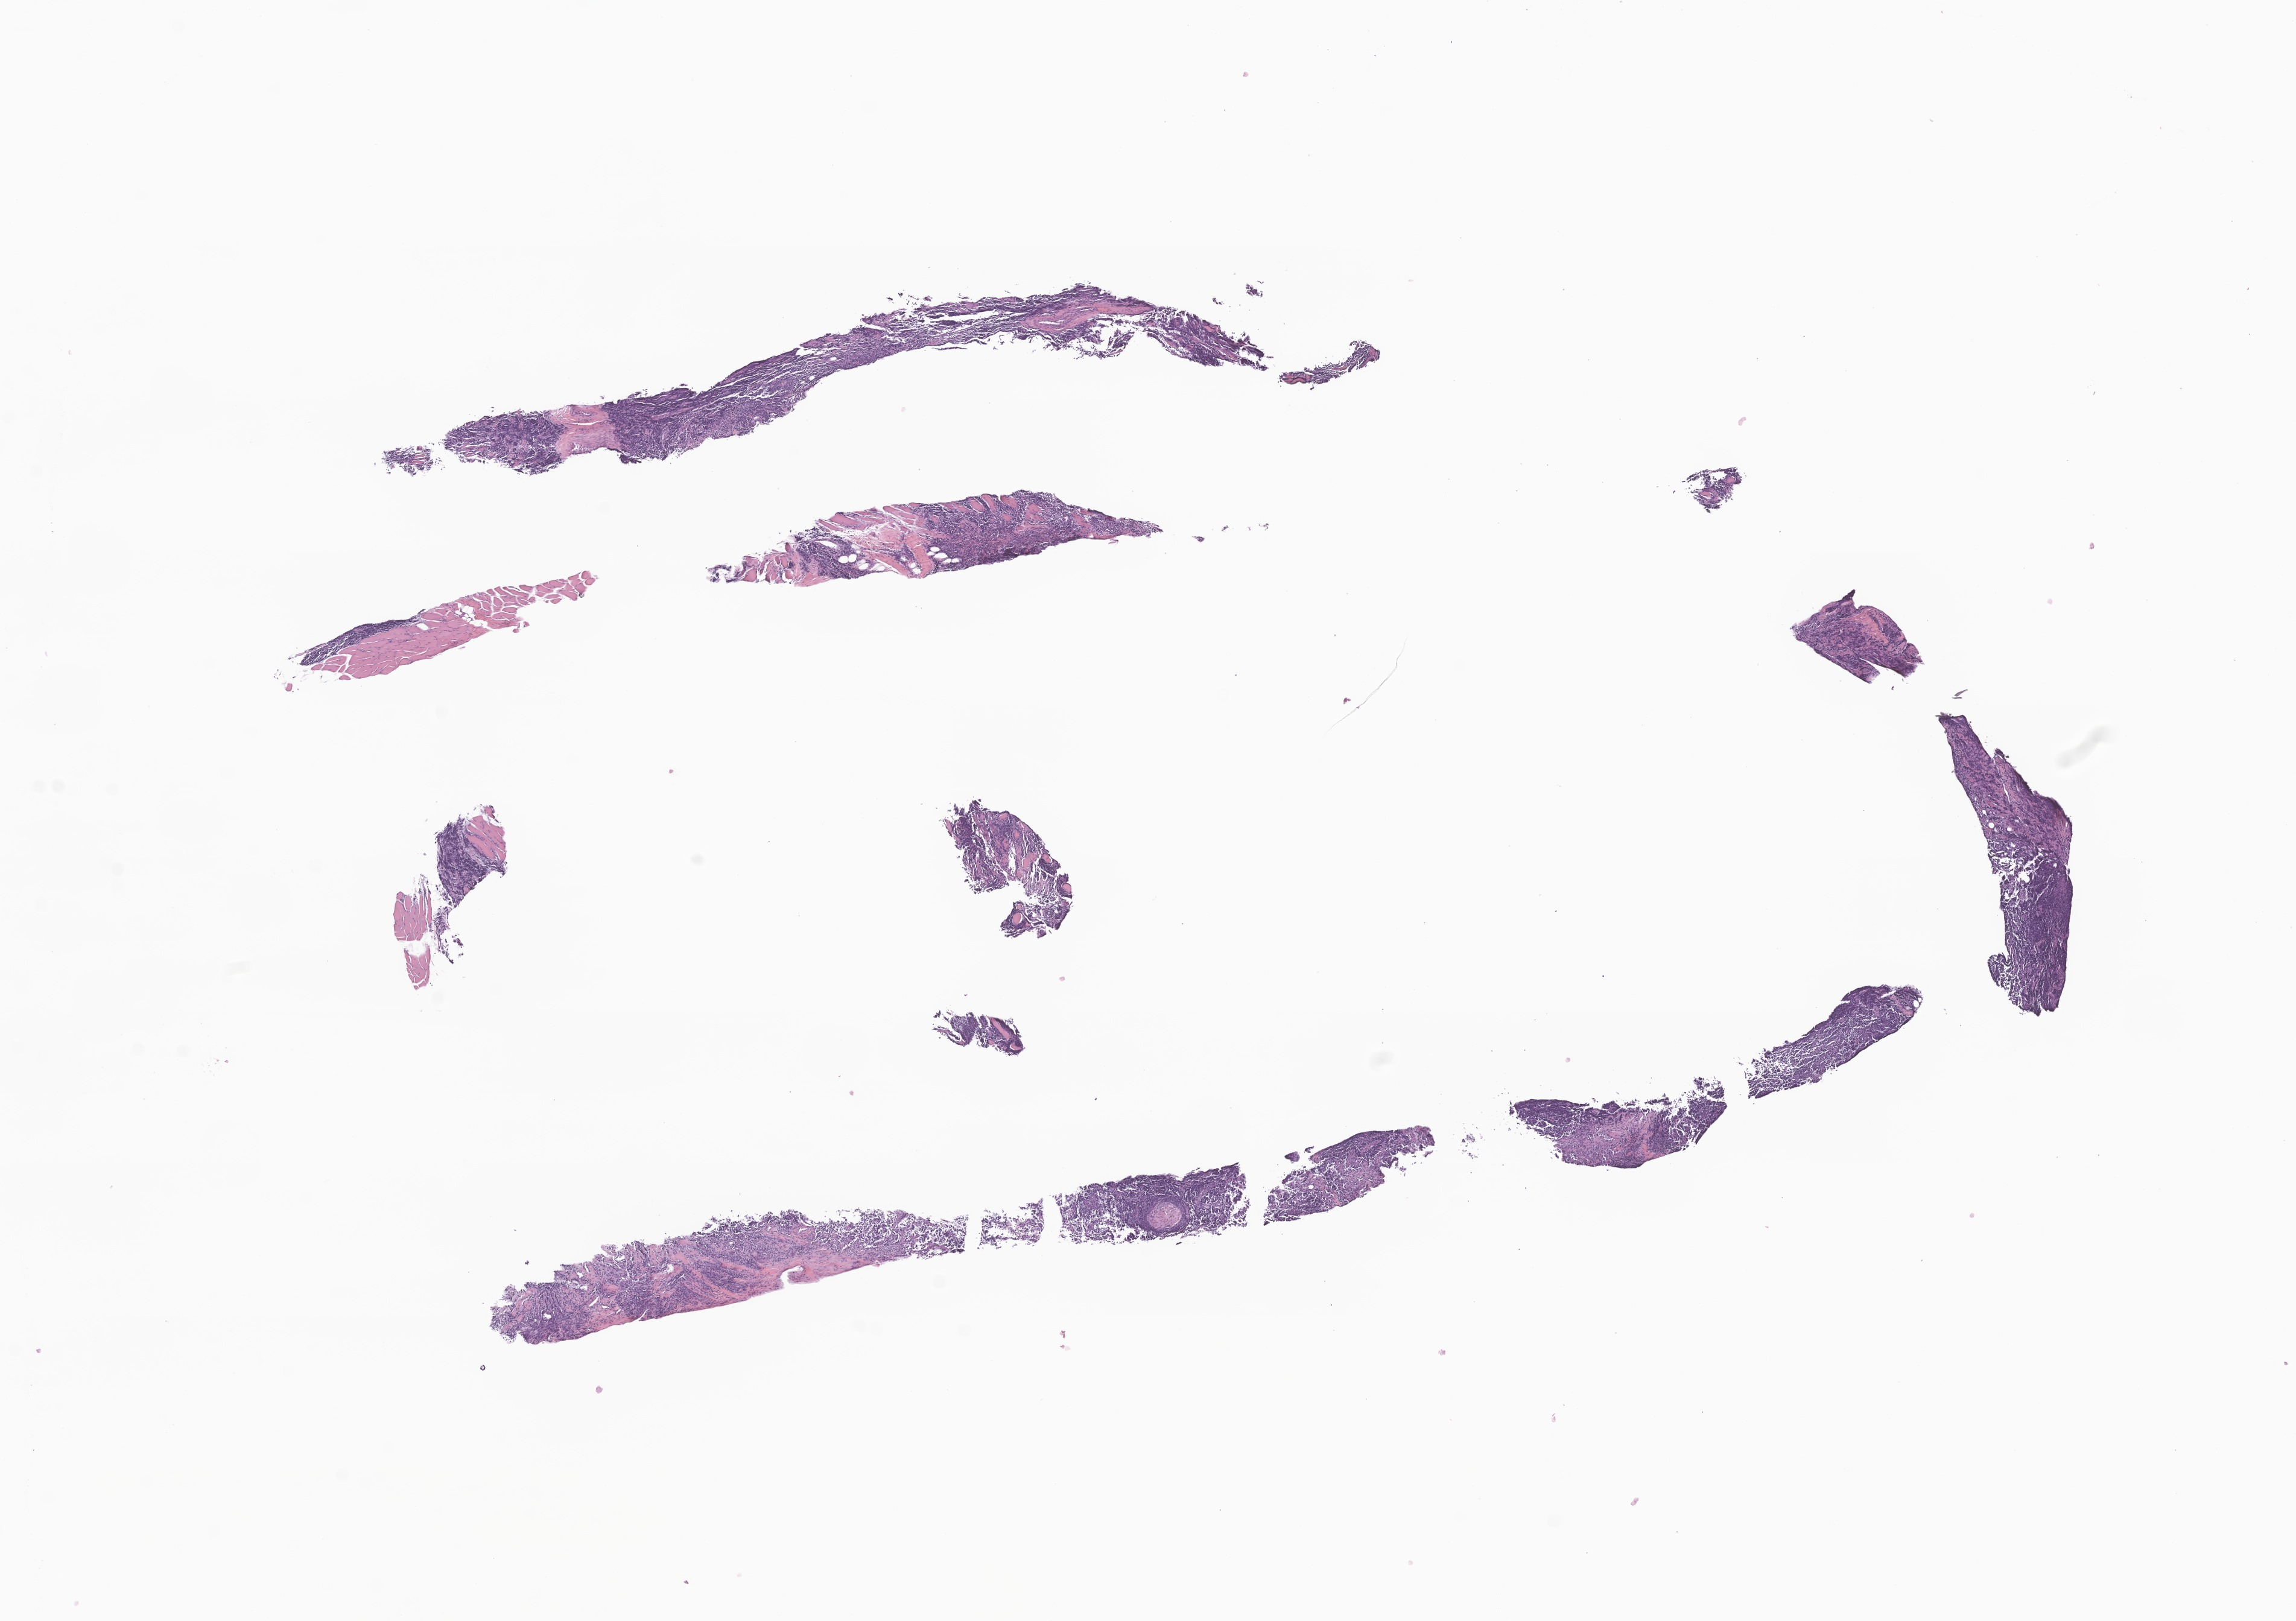
Whole-slide image, H&E stain of tumor tissue from the retroperitoneum — low-resolution overview of the scanned area, about 16.0 x 11.3 mm; formalin-fixed, paraffin-embedded (FFPE) tissue. Patient female; age 154 months (12 years 10 months).
Diagnosis: Rhabdomyosarcoma, NOS.